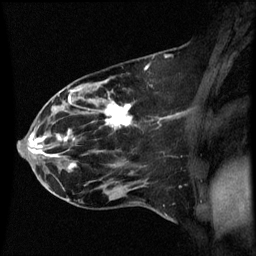
Breast MRI (dynamic contrast-enhanced), one sagittal slice. Position 25 of 60 along the scan axis. Dynamic contrast-enhanced series, image 2 of 3 at this slice position (ordered by acquisition). 1.5 T. TE 4.2 ms, TR 8.9 ms. 256 × 256 image matrix. Patient: female, 44 years. Case-level facts recorded for this patient, not image findings: setting: breast cancer imaged before/during neoadjuvant chemotherapy; receptor status: HR-positive, HER2-negative.
Outlined on this slice (semi-automatically segmented with operator editing):
- analysis volume of interest (the breast-tissue region the enhancement analysis was run in; not a lesion): box from (x=43, y=78) to (x=153, y=189) px
- tumour enhancement mask (voxels above the 70 % enhancement threshold inside the analysis volume of interest): (x=57, y=90)–(x=132, y=169)